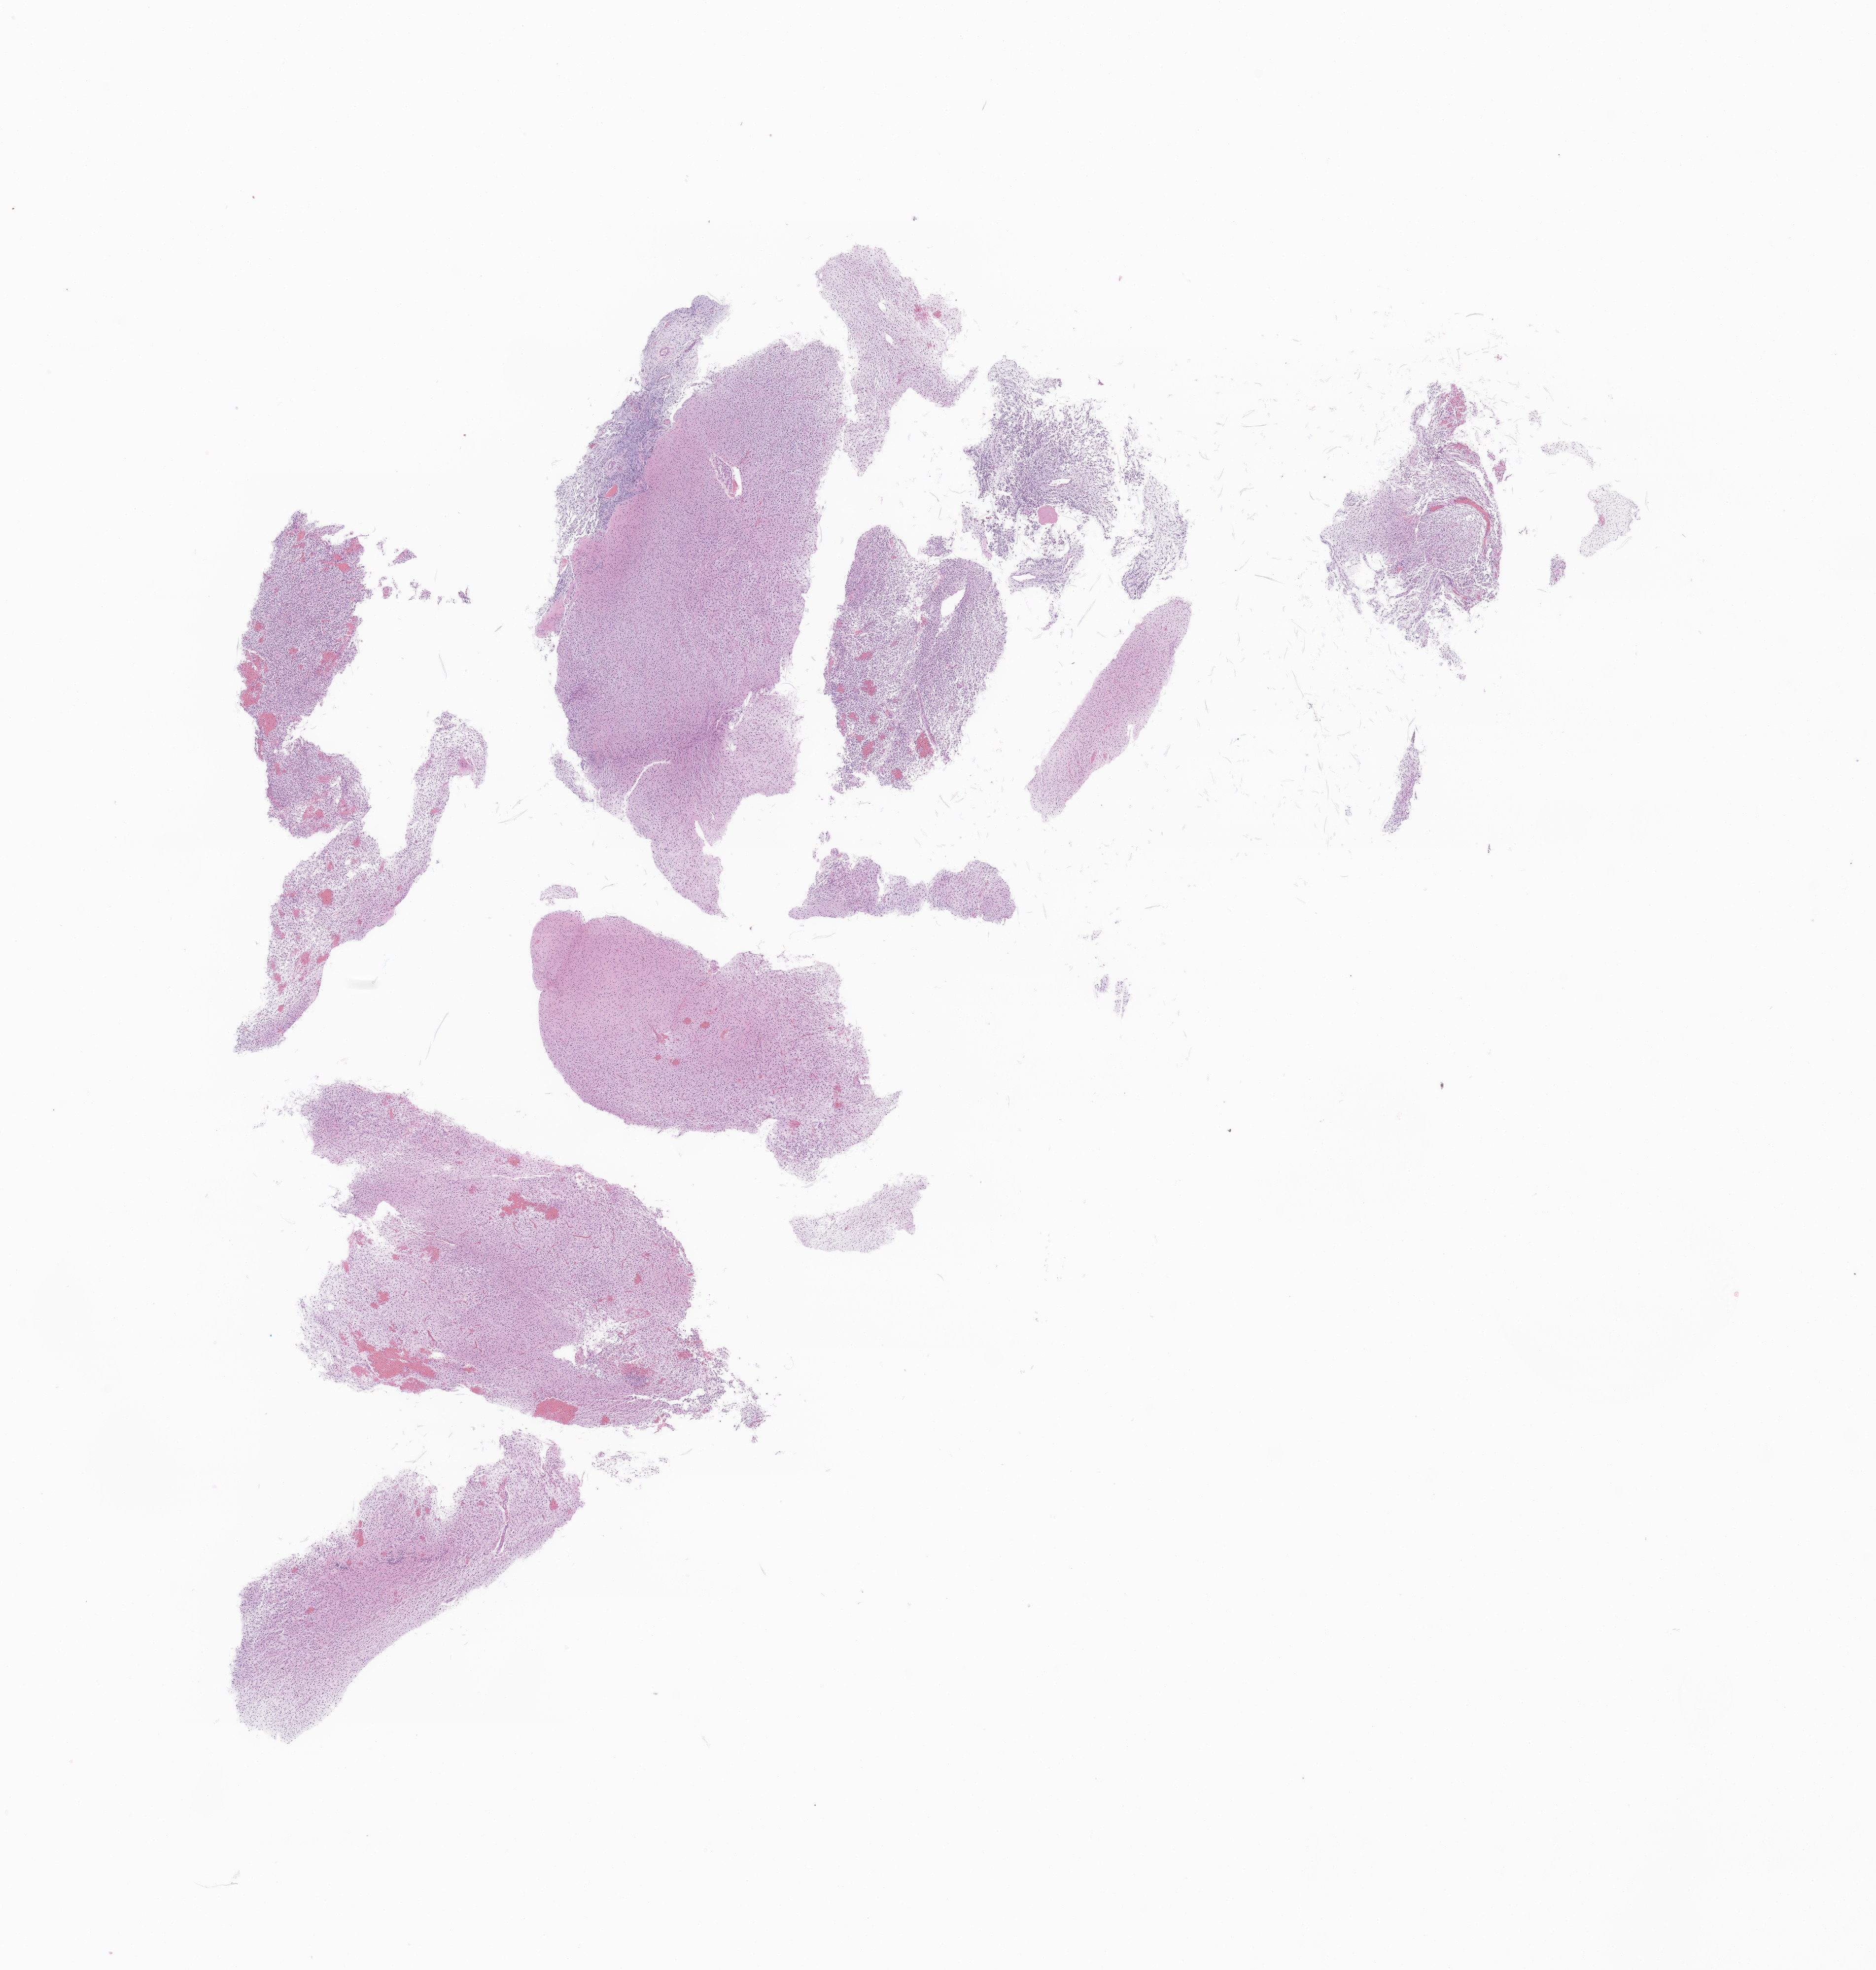
Digitized haematoxylin and eosin-stained section of tumor tissue from the brain stem — low-resolution overview of the scanned area, about 16.0 x 16.9 mm. FFPE section. Patient: female, age 95 days.
Recorded diagnosis: Neoplasm, malignant.